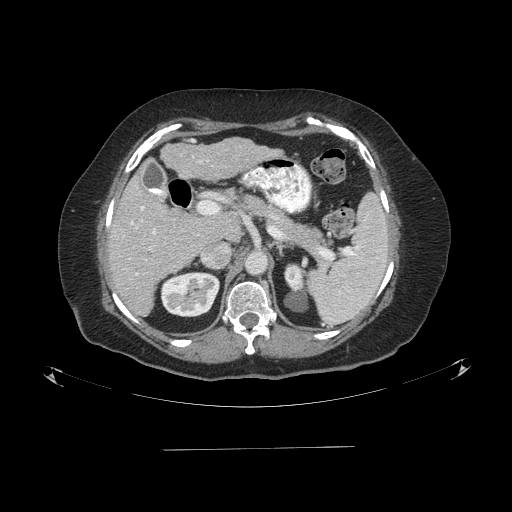
Contrast-enhanced abdominal CT (liver protocol), one axial slice. Slice 48 of 103 in the series (ordered by position). Reconstruction kernel STANDARD. One of 2 acquisitions stored at this slice position. Soft-tissue window (W 400 / L 40 HU). 2.5 mm slice thickness. 512 × 512 image matrix, field of view 500 × 500 mm. From the clinical record (not read from this slice): diagnosis: hepatocellular carcinoma (patient treated with transarterial chemoembolisation; whether this scan precedes or follows treatment is not stated here); TNM stage (as recorded): Stage-IIIA; Child-Pugh class: A; tumour nodularity: multinodular.
Structures marked on this image (semi-automatic segmentation, software-assisted and operator-edited):
- liver parenchyma outside the tumour (the mass and vessels are separate outlines, so this box may not span the whole liver): box from (x=107, y=138) to (x=278, y=316) px
- liver vessels: (x=130, y=161)–(x=202, y=276)